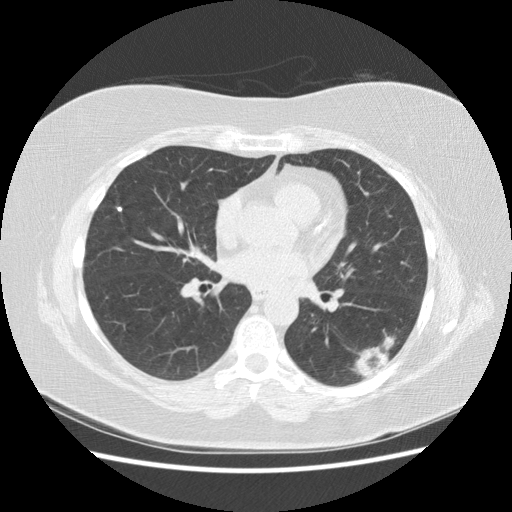
Low-dose screening chest CT, one axial slice. Slice 77 of 151 in the series (ordered by position). Lung window (W 1500 / L -600 HU). 512 × 512 image matrix, field of view 360 × 360 mm.
Annotated regions visible in this slice (manually delineated by an expert):
- lesion 1 (tumor, lower lobe of left lung): bounding box [x1, y1, x2, y2] px = [355, 336, 395, 377]